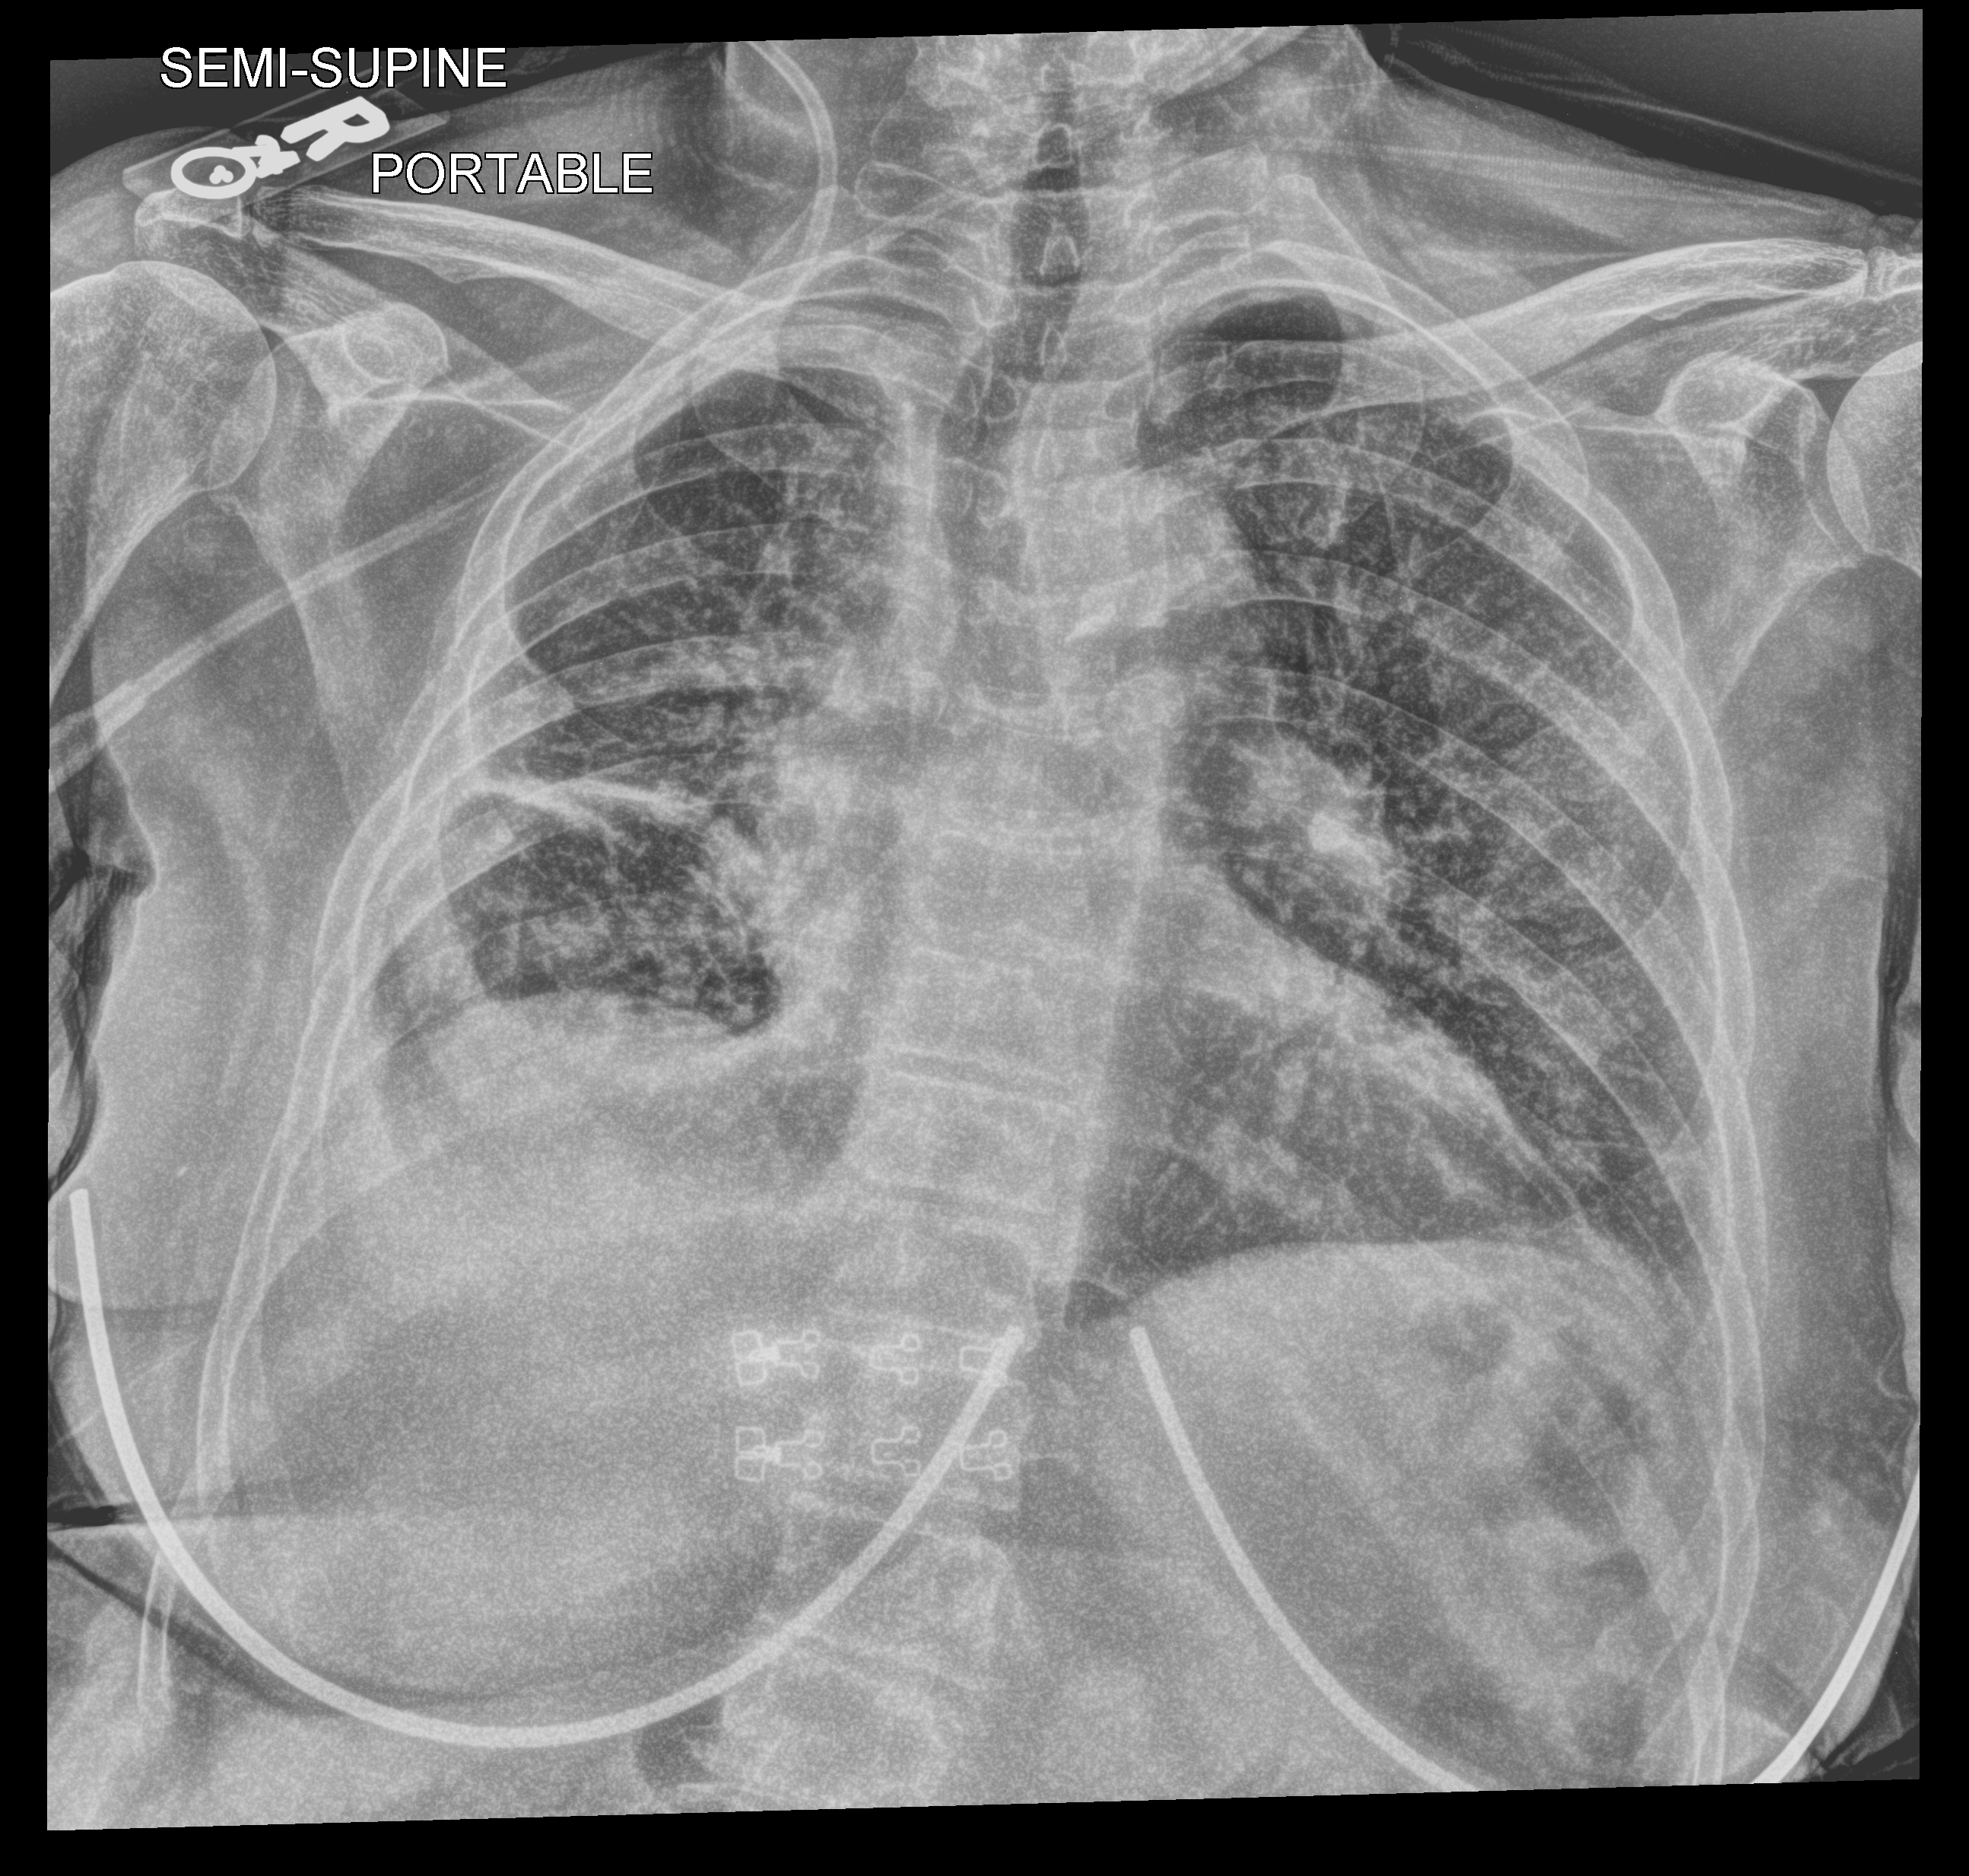
Portable chest radiograph, anteroposterior (AP) projection. Female patient hospitalised with COVID-19, age 60–74 years.
Admission-level facts for this patient (not findings on this image; timing relative to this image not recorded):
- admitted to intensive care during this hospital stay: no